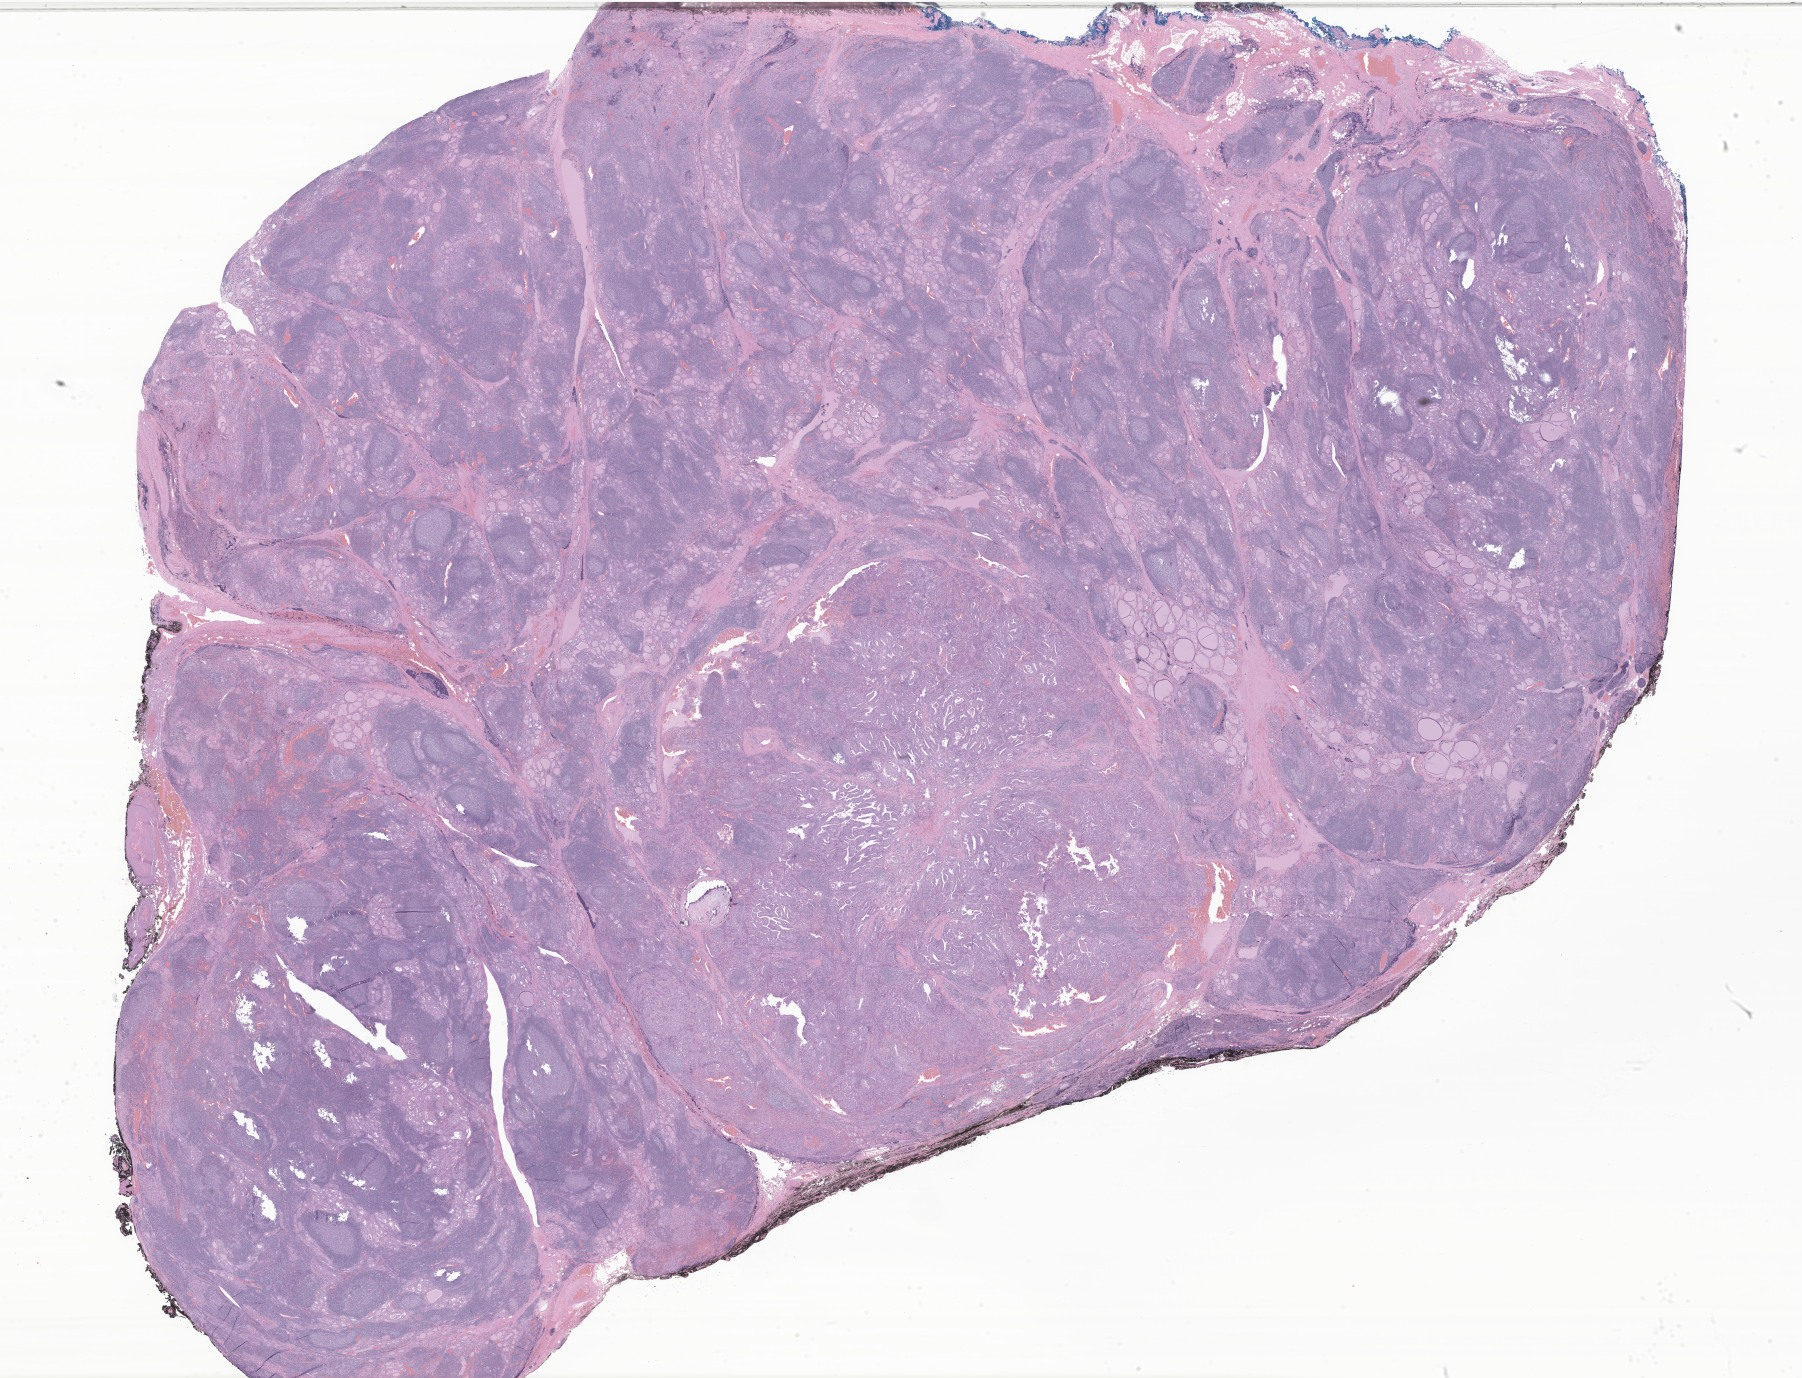
Haematoxylin and eosin whole-slide image of tumor tissue from the thyroid — low-resolution overview of the scanned area, about 30.4 x 23.2 mm, FFPE section. Patient: female, age 175 months (14 years 7 months).
Diagnosis (ICD-O-3 morphology term): Carcinoma, NOS.